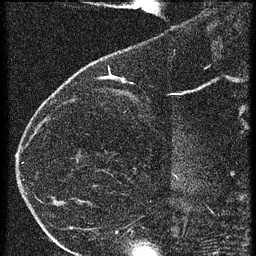
Breast MRI (dynamic contrast-enhanced), one sagittal slice; slice 16 of 60 in the series (ordered by position); 3 images stored at this slice position (order not interpretable as contrast timing); 1.5 T; TE 4.2 ms, TR 20.4 ms; 1.5 mm slice thickness; 256 × 256 image matrix, field of view 180 × 180 mm. Patient: female, 35 years. From the clinical record (not read from this slice): setting: breast cancer imaged before/during neoadjuvant chemotherapy; receptor status: HR-positive, HER2-negative.
Structures marked on this image (semi-automatically segmented with operator editing):
- analysis volume of interest (the breast-tissue region the enhancement analysis was run in; not a lesion): bounding box <65,60,169,119> (left, top, right, bottom; pixels)
- tumour enhancement mask (voxels above the 90 % enhancement threshold inside the analysis volume of interest): <121,78,124,81>